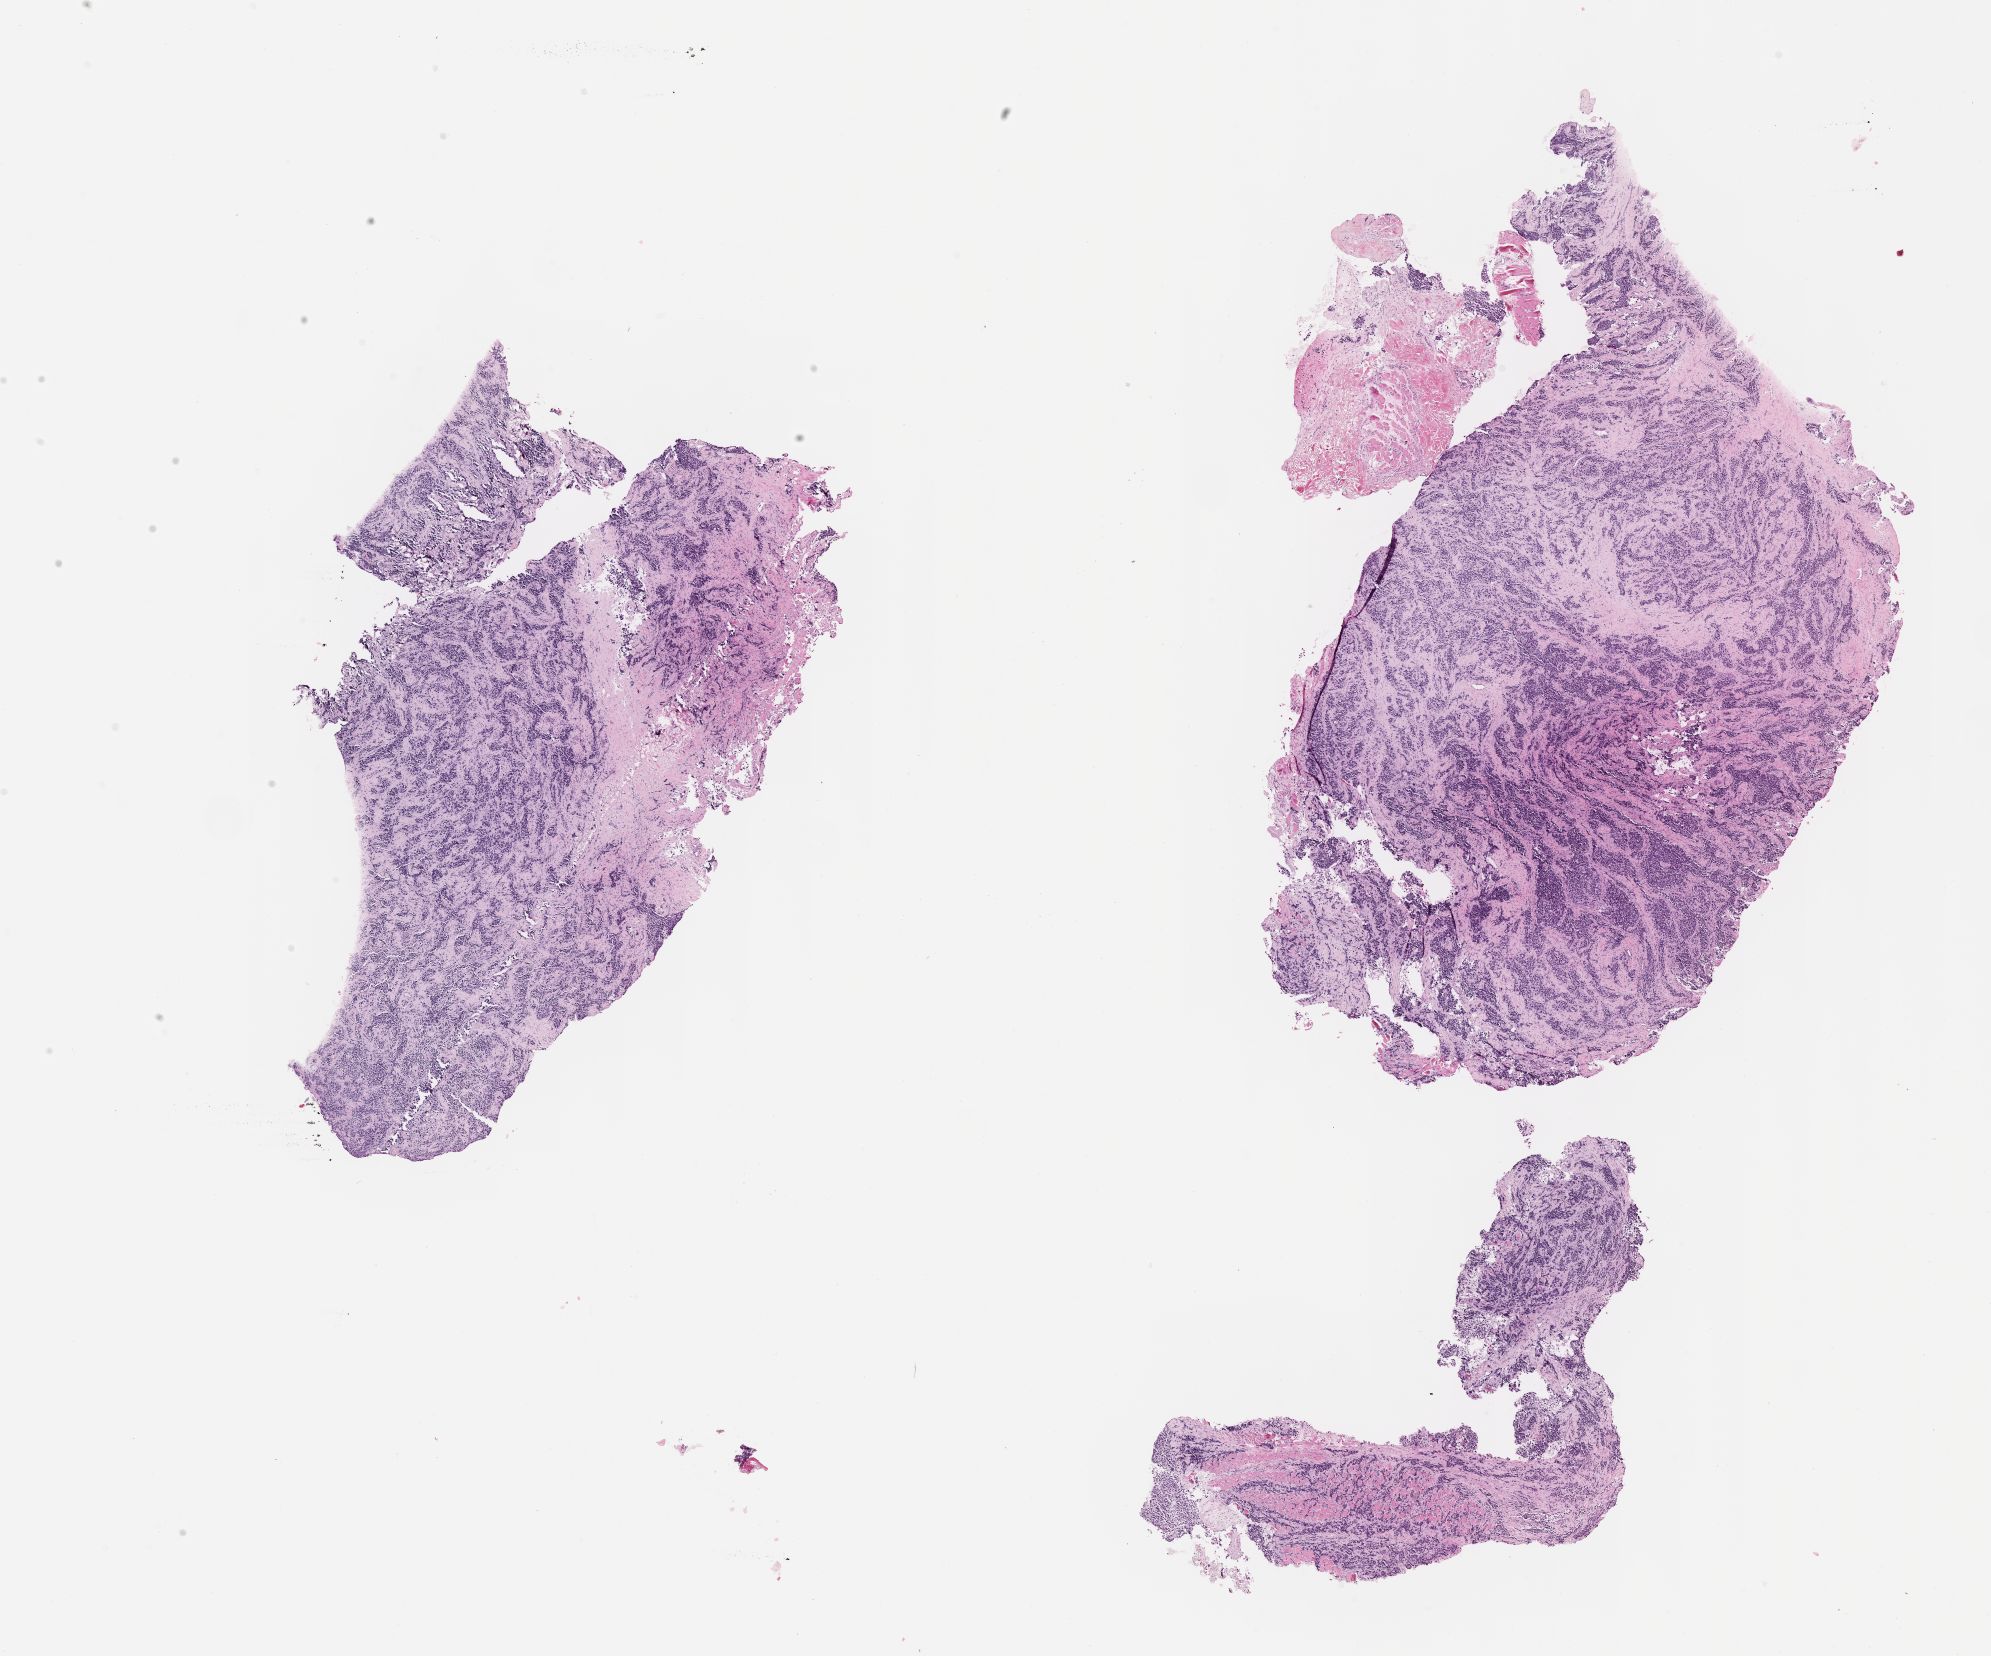
Haematoxylin and eosin whole-slide image of tumor tissue, low-resolution overview of the scanned area, about 16.1 x 13.4 mm. Formalin-fixed paraffin-embedded section. Sample anatomic site: soft tissue - calf, left. Female patient, age at diagnosis 3.2 years.
Diagnosis: rhabdomyosarcoma; histological classification: alveolar rhabdomyosarcoma. Stage (as recorded): 4. Metastatic status at presentation (as recorded): metastatic.